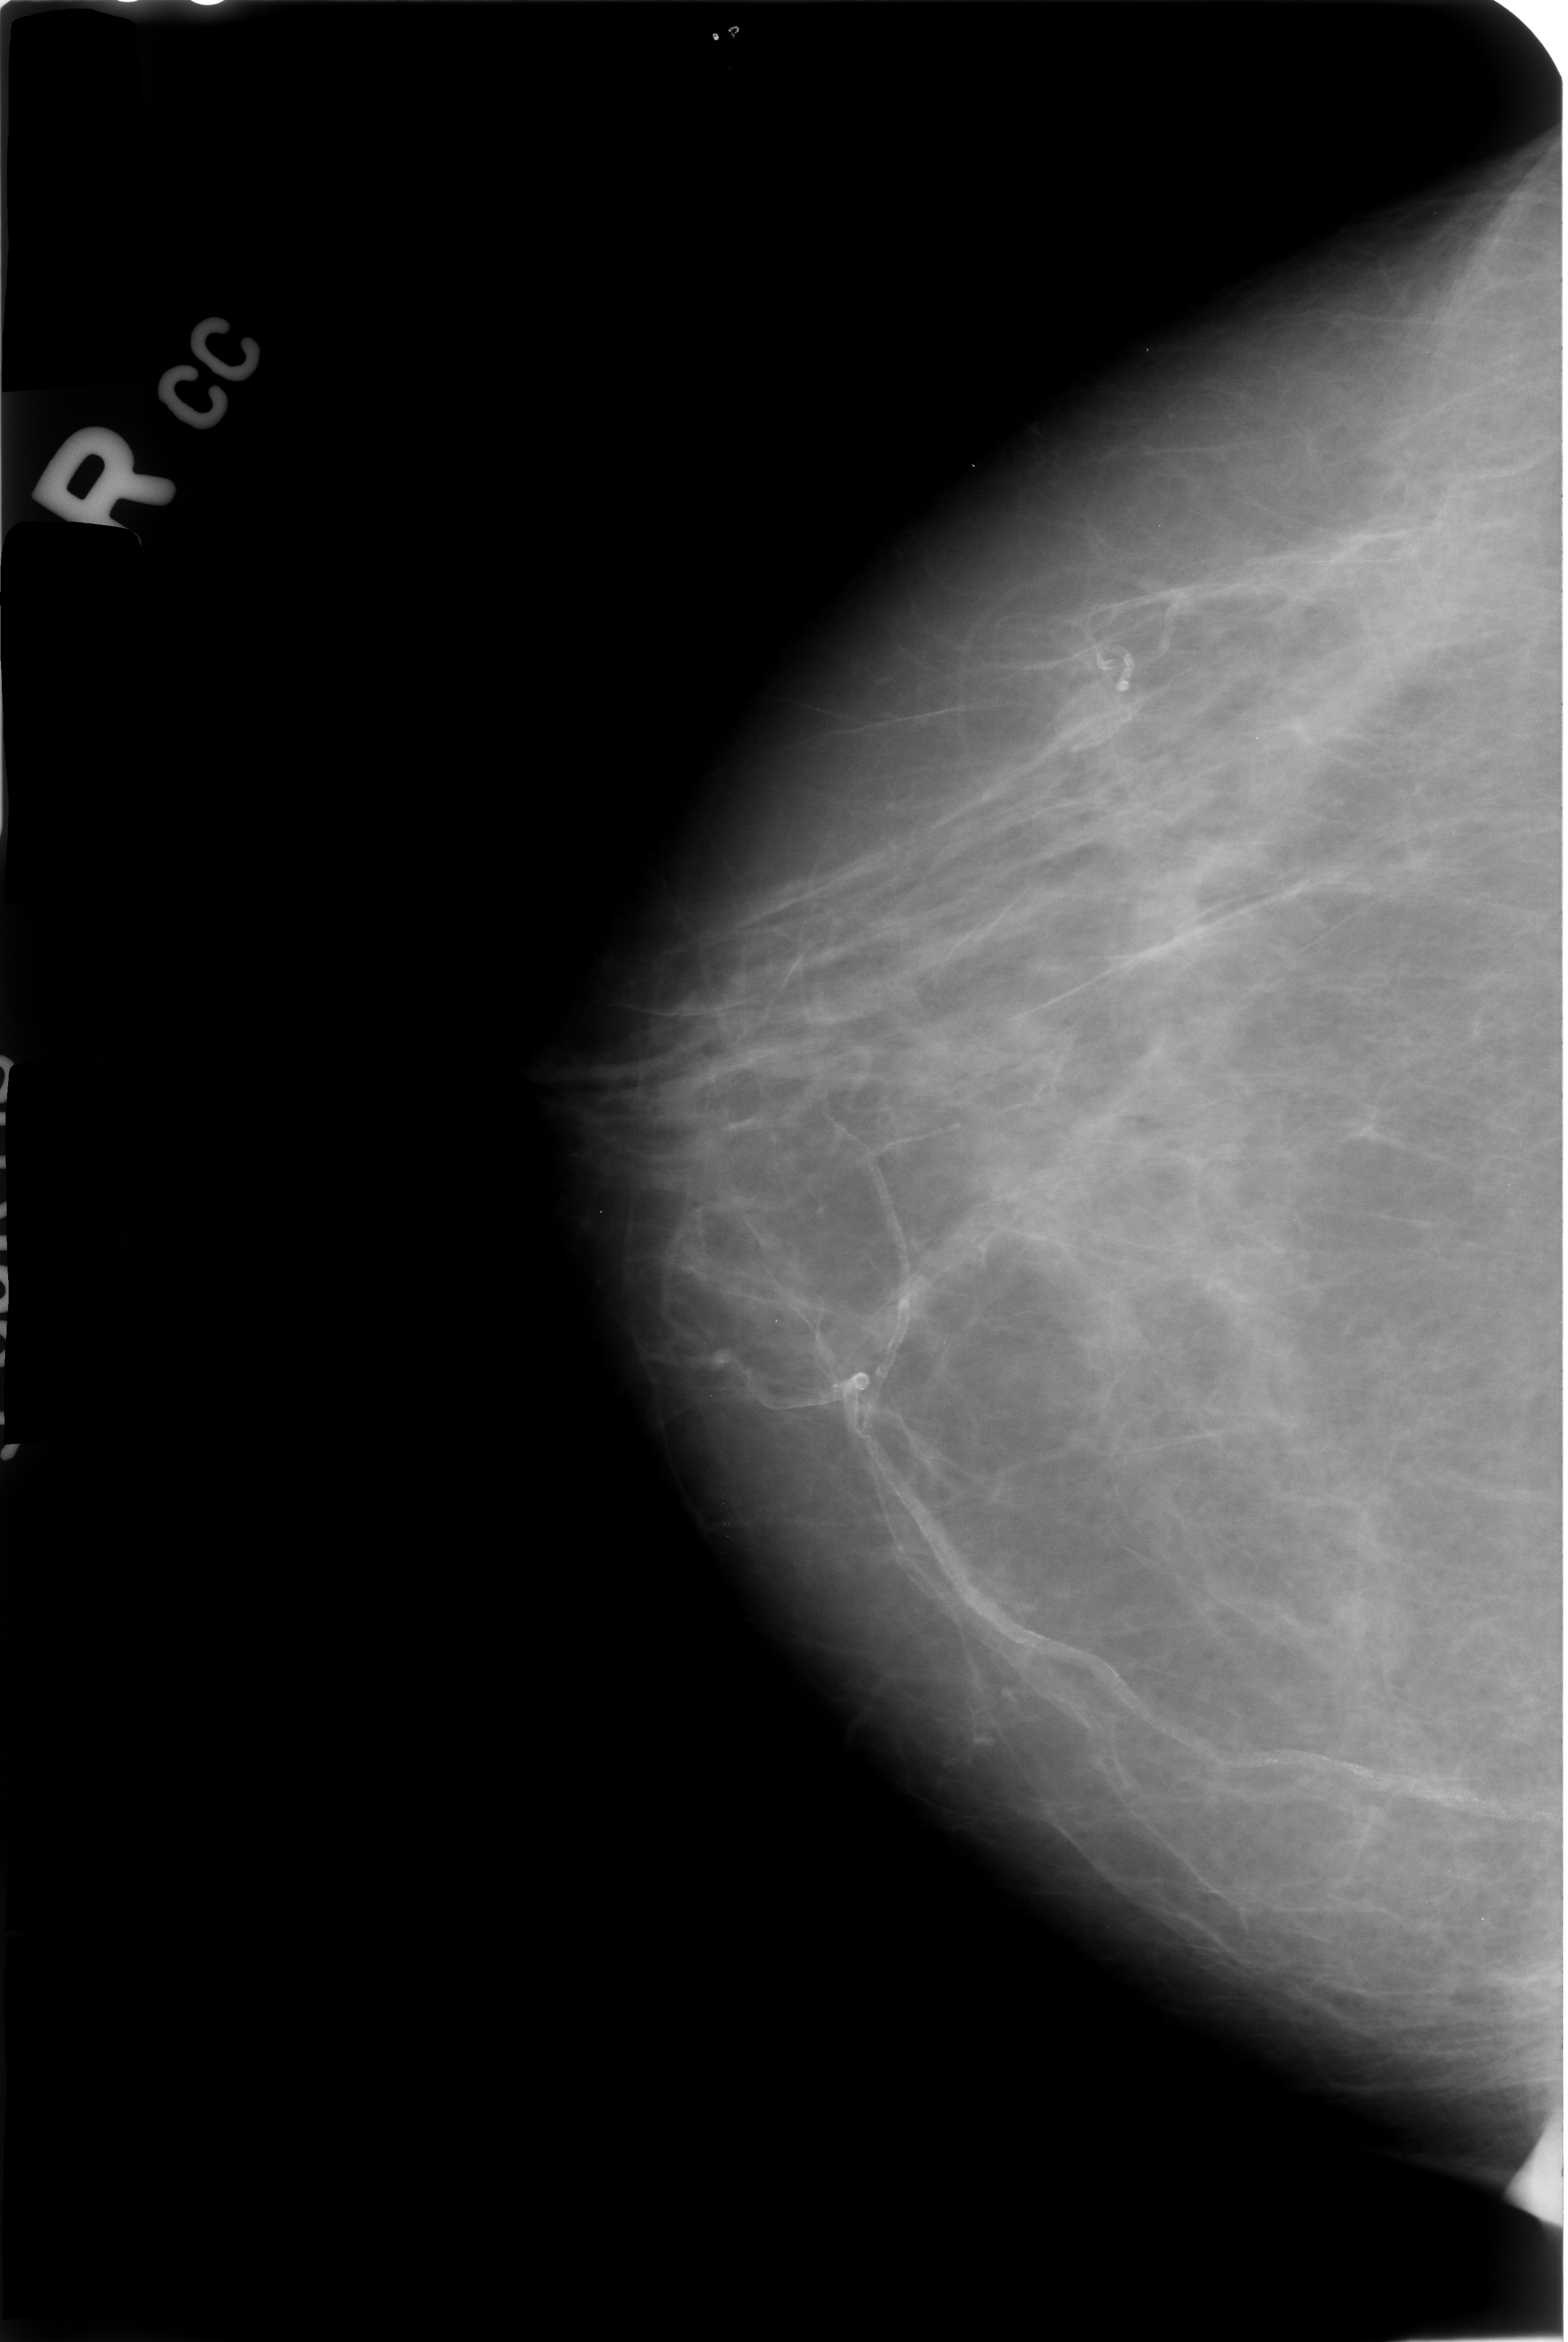
Mammogram (digitized film); right breast; CC view; breast composition: scattered fibroglandular densities (BI-RADS density category 2 of 4); 1568 × 2342 image matrix.
Expert-marked regions of interest on this image (one box per marked abnormality):
- Finding 1 of 2: calcifications, morphology vascular; BI-RADS assessment category 2; outcome (as recorded, no biopsy): benign without callback (not worked up further): bounding box (x1, y1, x2, y2) in pixels: (709, 1162, 1561, 1845)
- Finding 2 of 2: calcifications, morphology vascular; BI-RADS assessment category 2; subtlety rating 3 on a 1 (subtle) to 5 (obvious) scale; outcome (as recorded, no biopsy): benign without callback (not worked up further): (777, 461, 1528, 913)